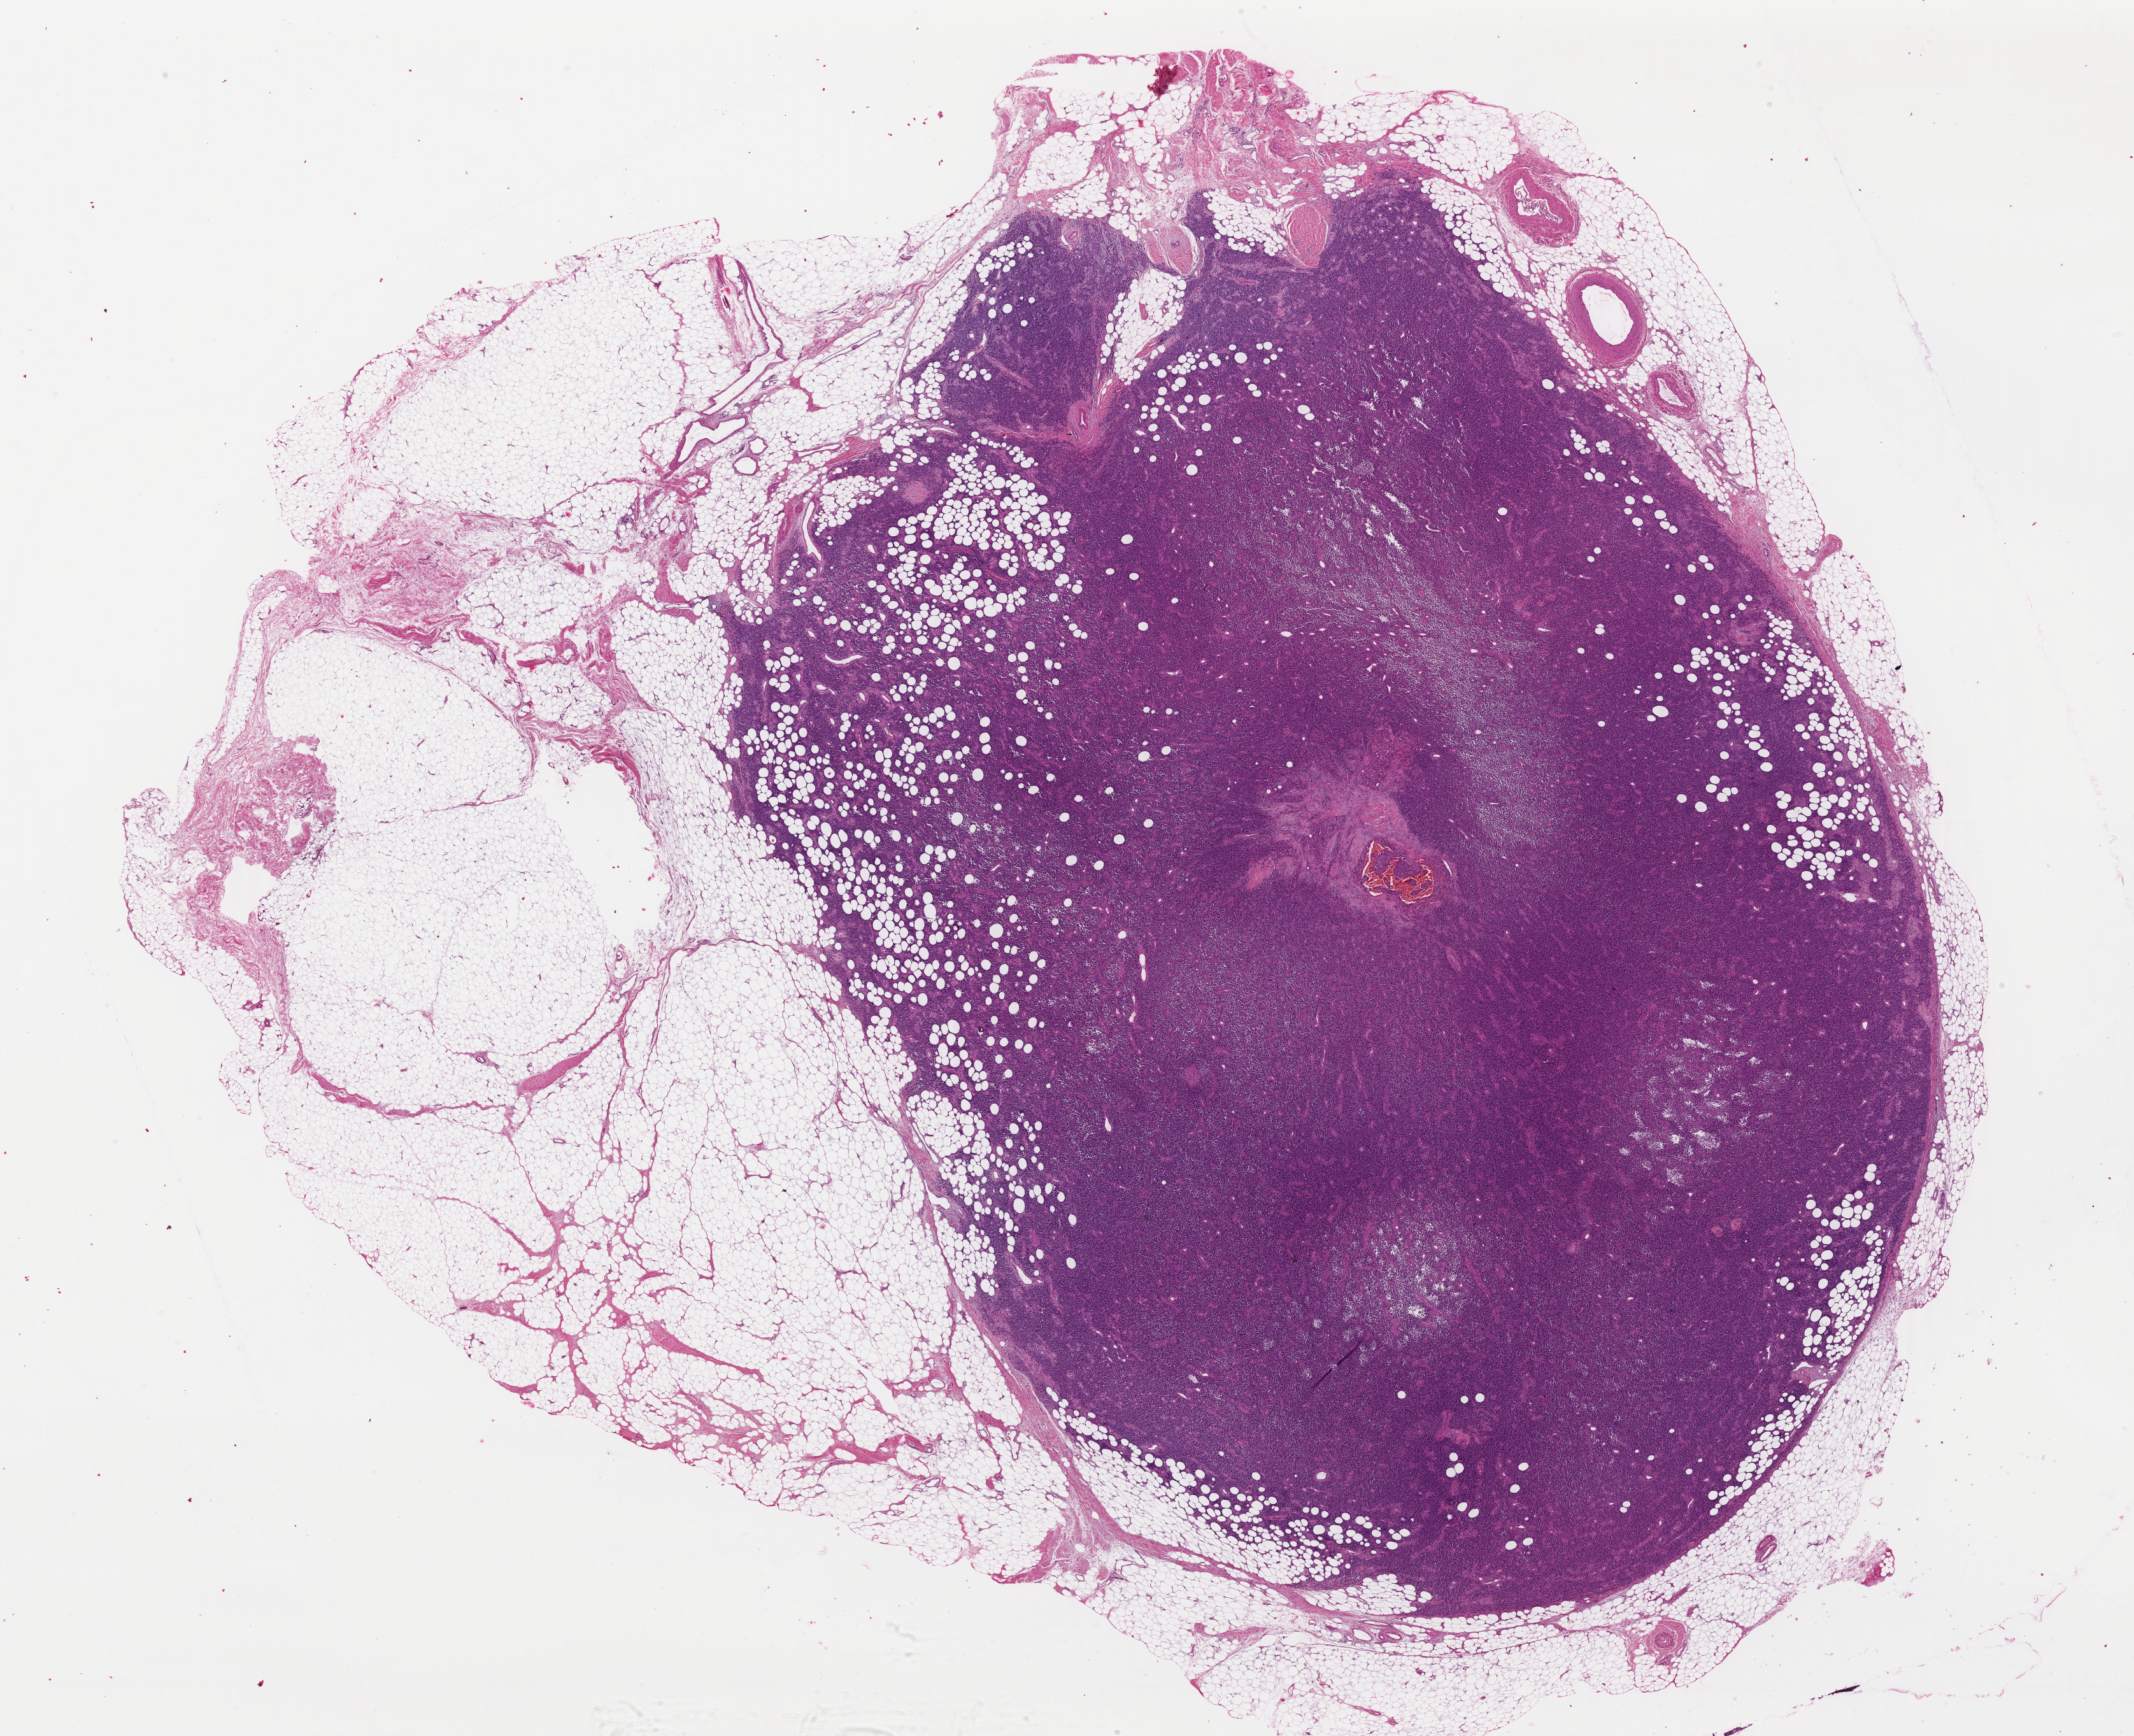
Hematoxylin and eosin (H&E) stained whole-slide image — low-resolution overview of the scanned area, about 26.7 x 21.7 mm (slide scanned at 40x), FFPE section, sample: primary tumour, skin. Male, age 42 years at initial diagnosis.
Pathologic diagnosis: Malignant melanoma, NOS.